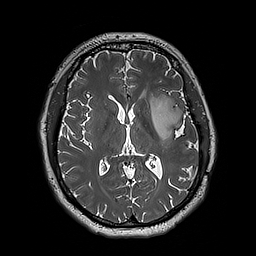
Brain MRI from a brain-tumour surgery series, one axial slice; position 100 of 192 along the scan axis; 1 mm slice thickness; 256 × 256 image matrix, field of view 250 × 250 mm. From the clinical record (not read from this slice): histopathology: Astrocytoma; WHO grade: 3; IDH mutation: yes; tumour location: Left Insular.
Outlined on this slice (outlined manually by an expert reader):
- tumour: bounding box [x1, y1, x2, y2] px = [149, 96, 184, 141]